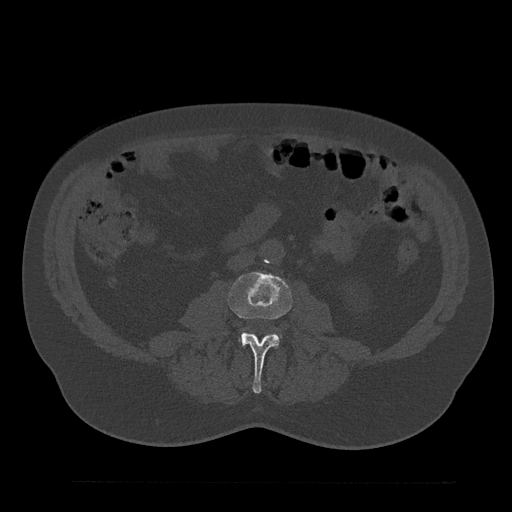
CT including the spine, one axial slice; position 16 of 797 along the scan axis; reconstruction kernel Br40s/3; 120 kVp; bone window (W 1800 / L 400 HU); 512 × 512 image matrix, field of view 430 × 430 mm. Patient: male, 61 years. Case-level facts recorded for this patient, not image findings: primary cancer: prostate.
Outlined on this slice (semi-automatic segmentation, software-assisted and operator-edited):
- L3 vertebra: bounding box [x1, y1, x2, y2] px = [228, 272, 292, 394]
- L4 vertebra: [241, 338, 243, 344]